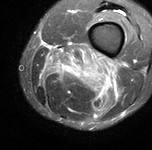
MRI of an extremity soft-tissue mass, one axial slice; slice 23 of 90 in the series (ordered by position); STIR; MR volume resampled by the dataset authors to the PET/CT grid (not the native acquisition matrix); 3.27 mm slice thickness; 152 × 150 image matrix, field of view 148 × 146 mm. Male patient. Case-level facts recorded for this patient, not image findings: histological type: undifferentiated pleomorphic liposarcoma; grade: high; site of the primary tumour: left thigh.
Annotated regions visible in this slice (expert contour drawn on MRI and transferred to this co-registered scan by the dataset authors):
- gross tumour volume including surrounding oedema: box from (x=41, y=44) to (x=124, y=90) px